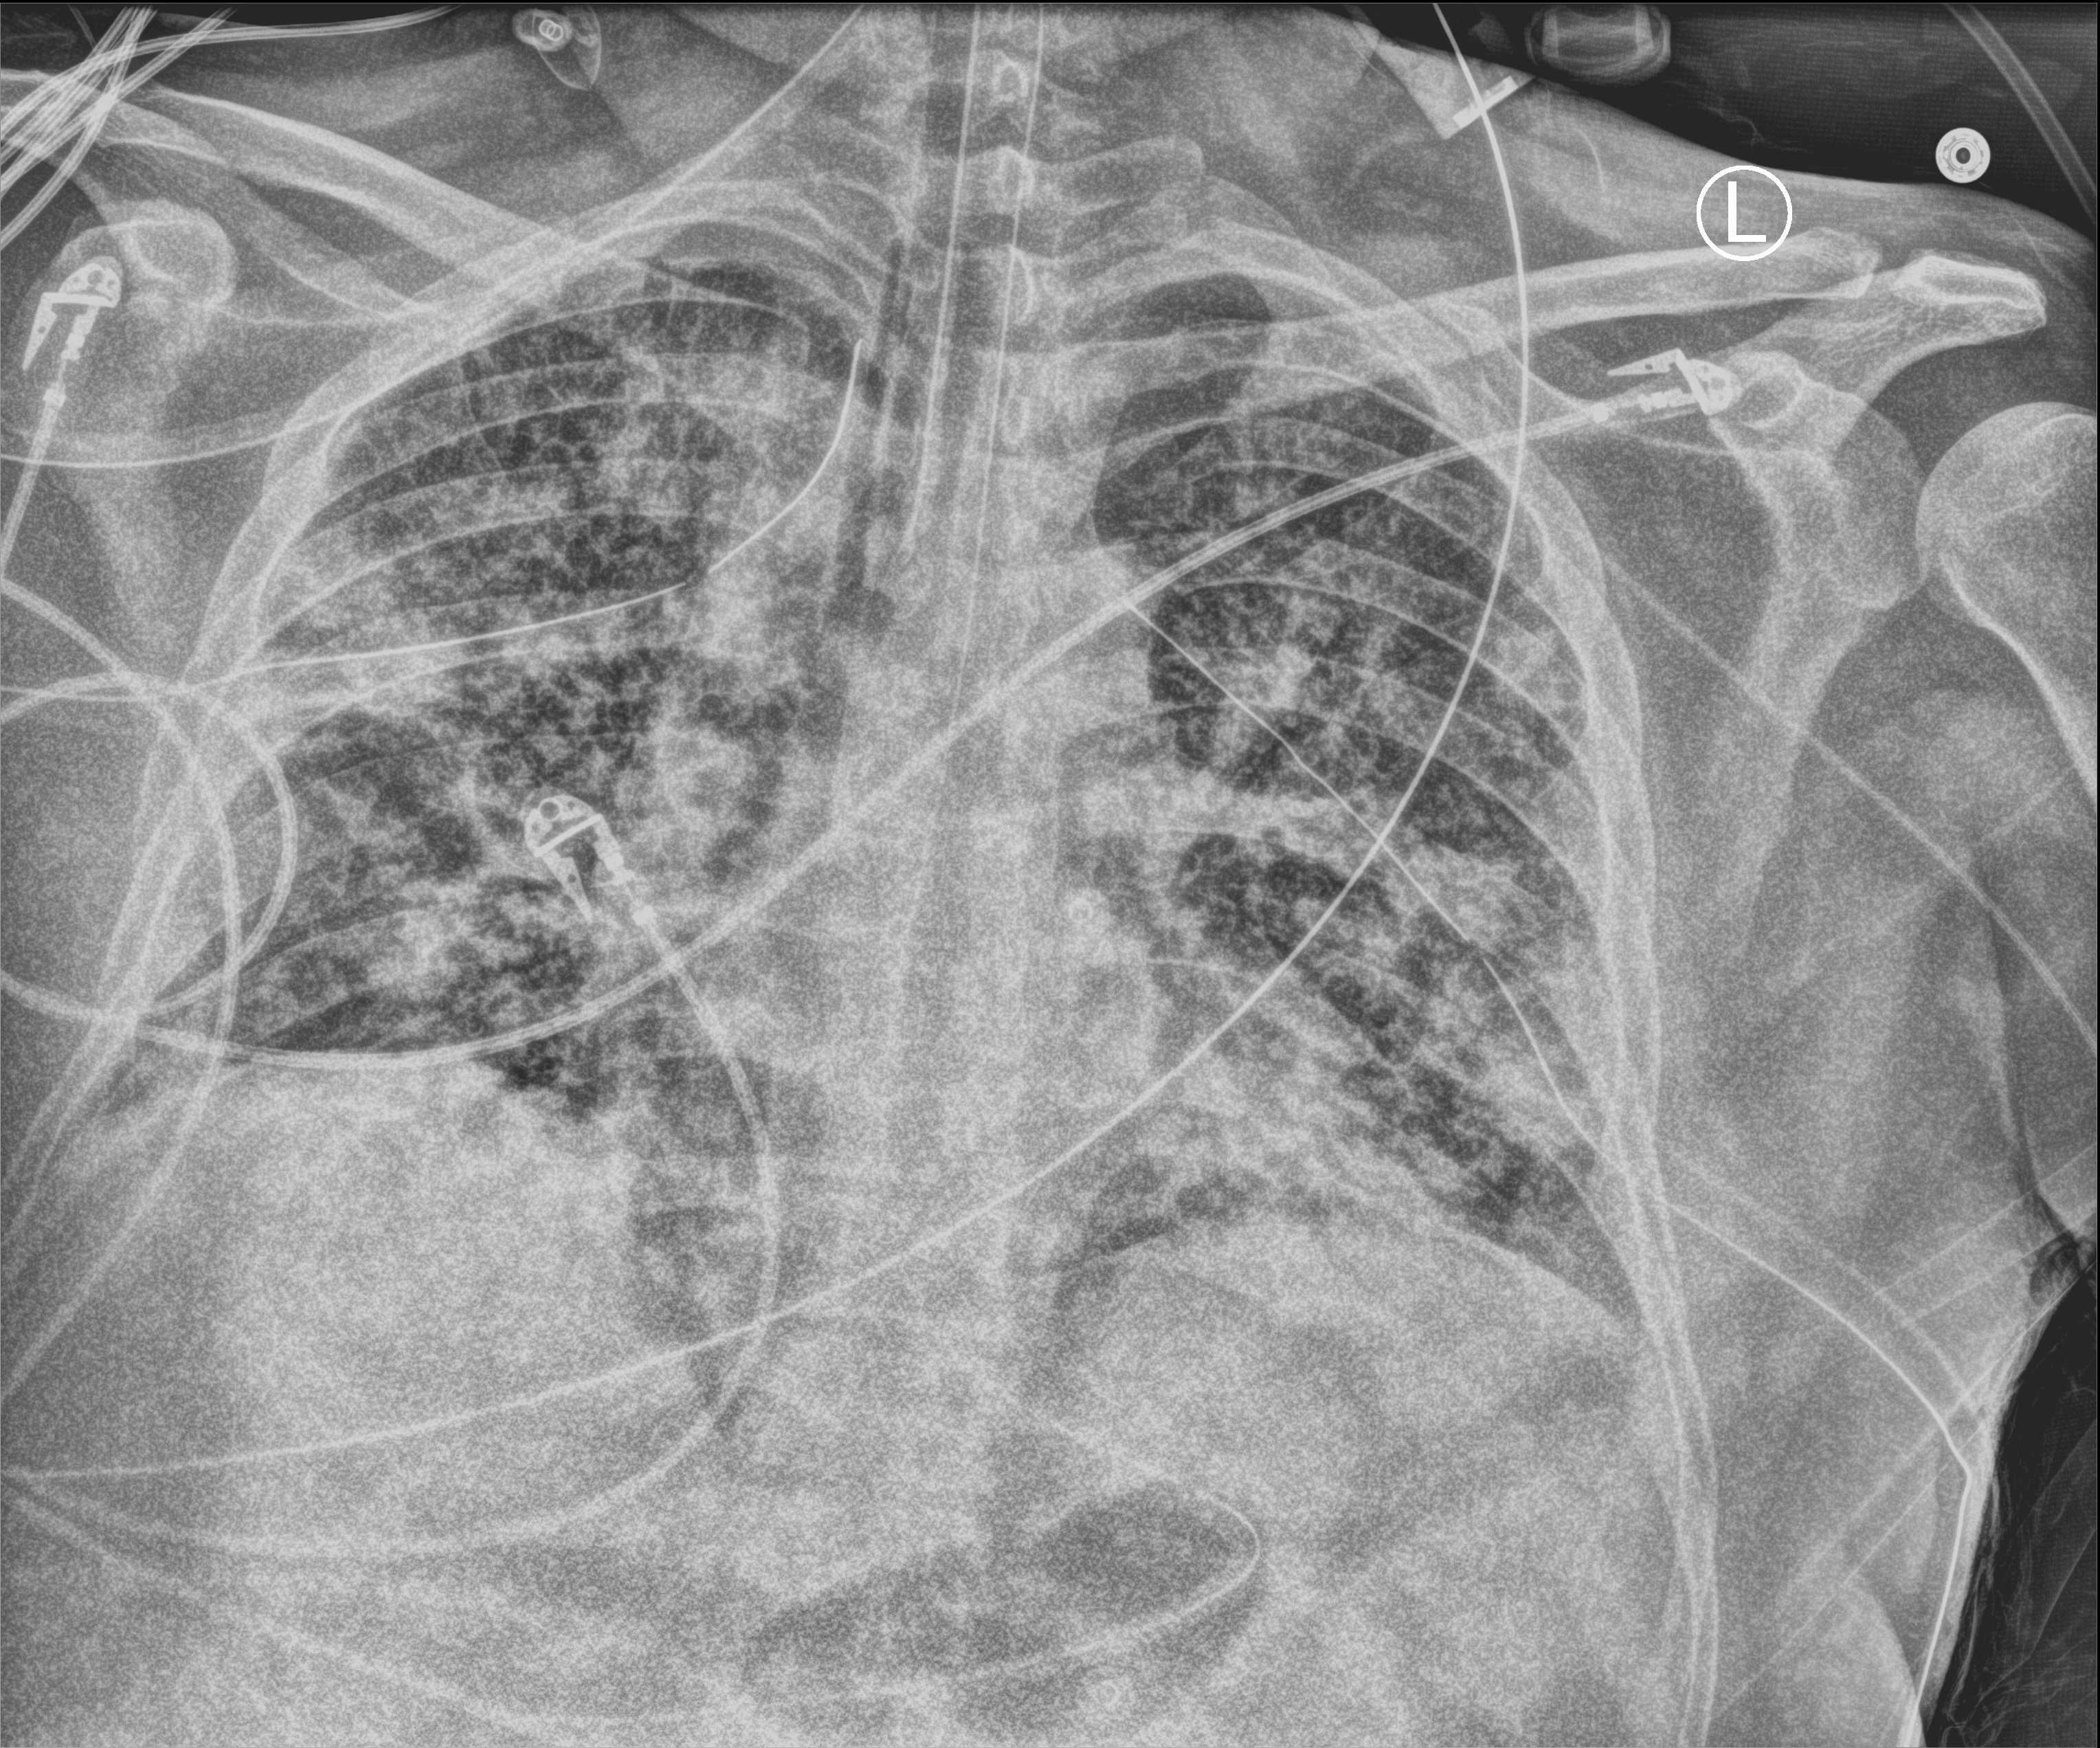
Chest X-ray (portable); anteroposterior (AP) projection. Patient hospitalised with COVID-19; male, aged 18–59 years.
From the hospital-stay record, not from the radiograph (when in the stay this image was taken is not recorded): mechanically ventilated during this hospital stay: yes; length of hospital stay: 63 days; admitted to intensive care during this hospital stay: yes.